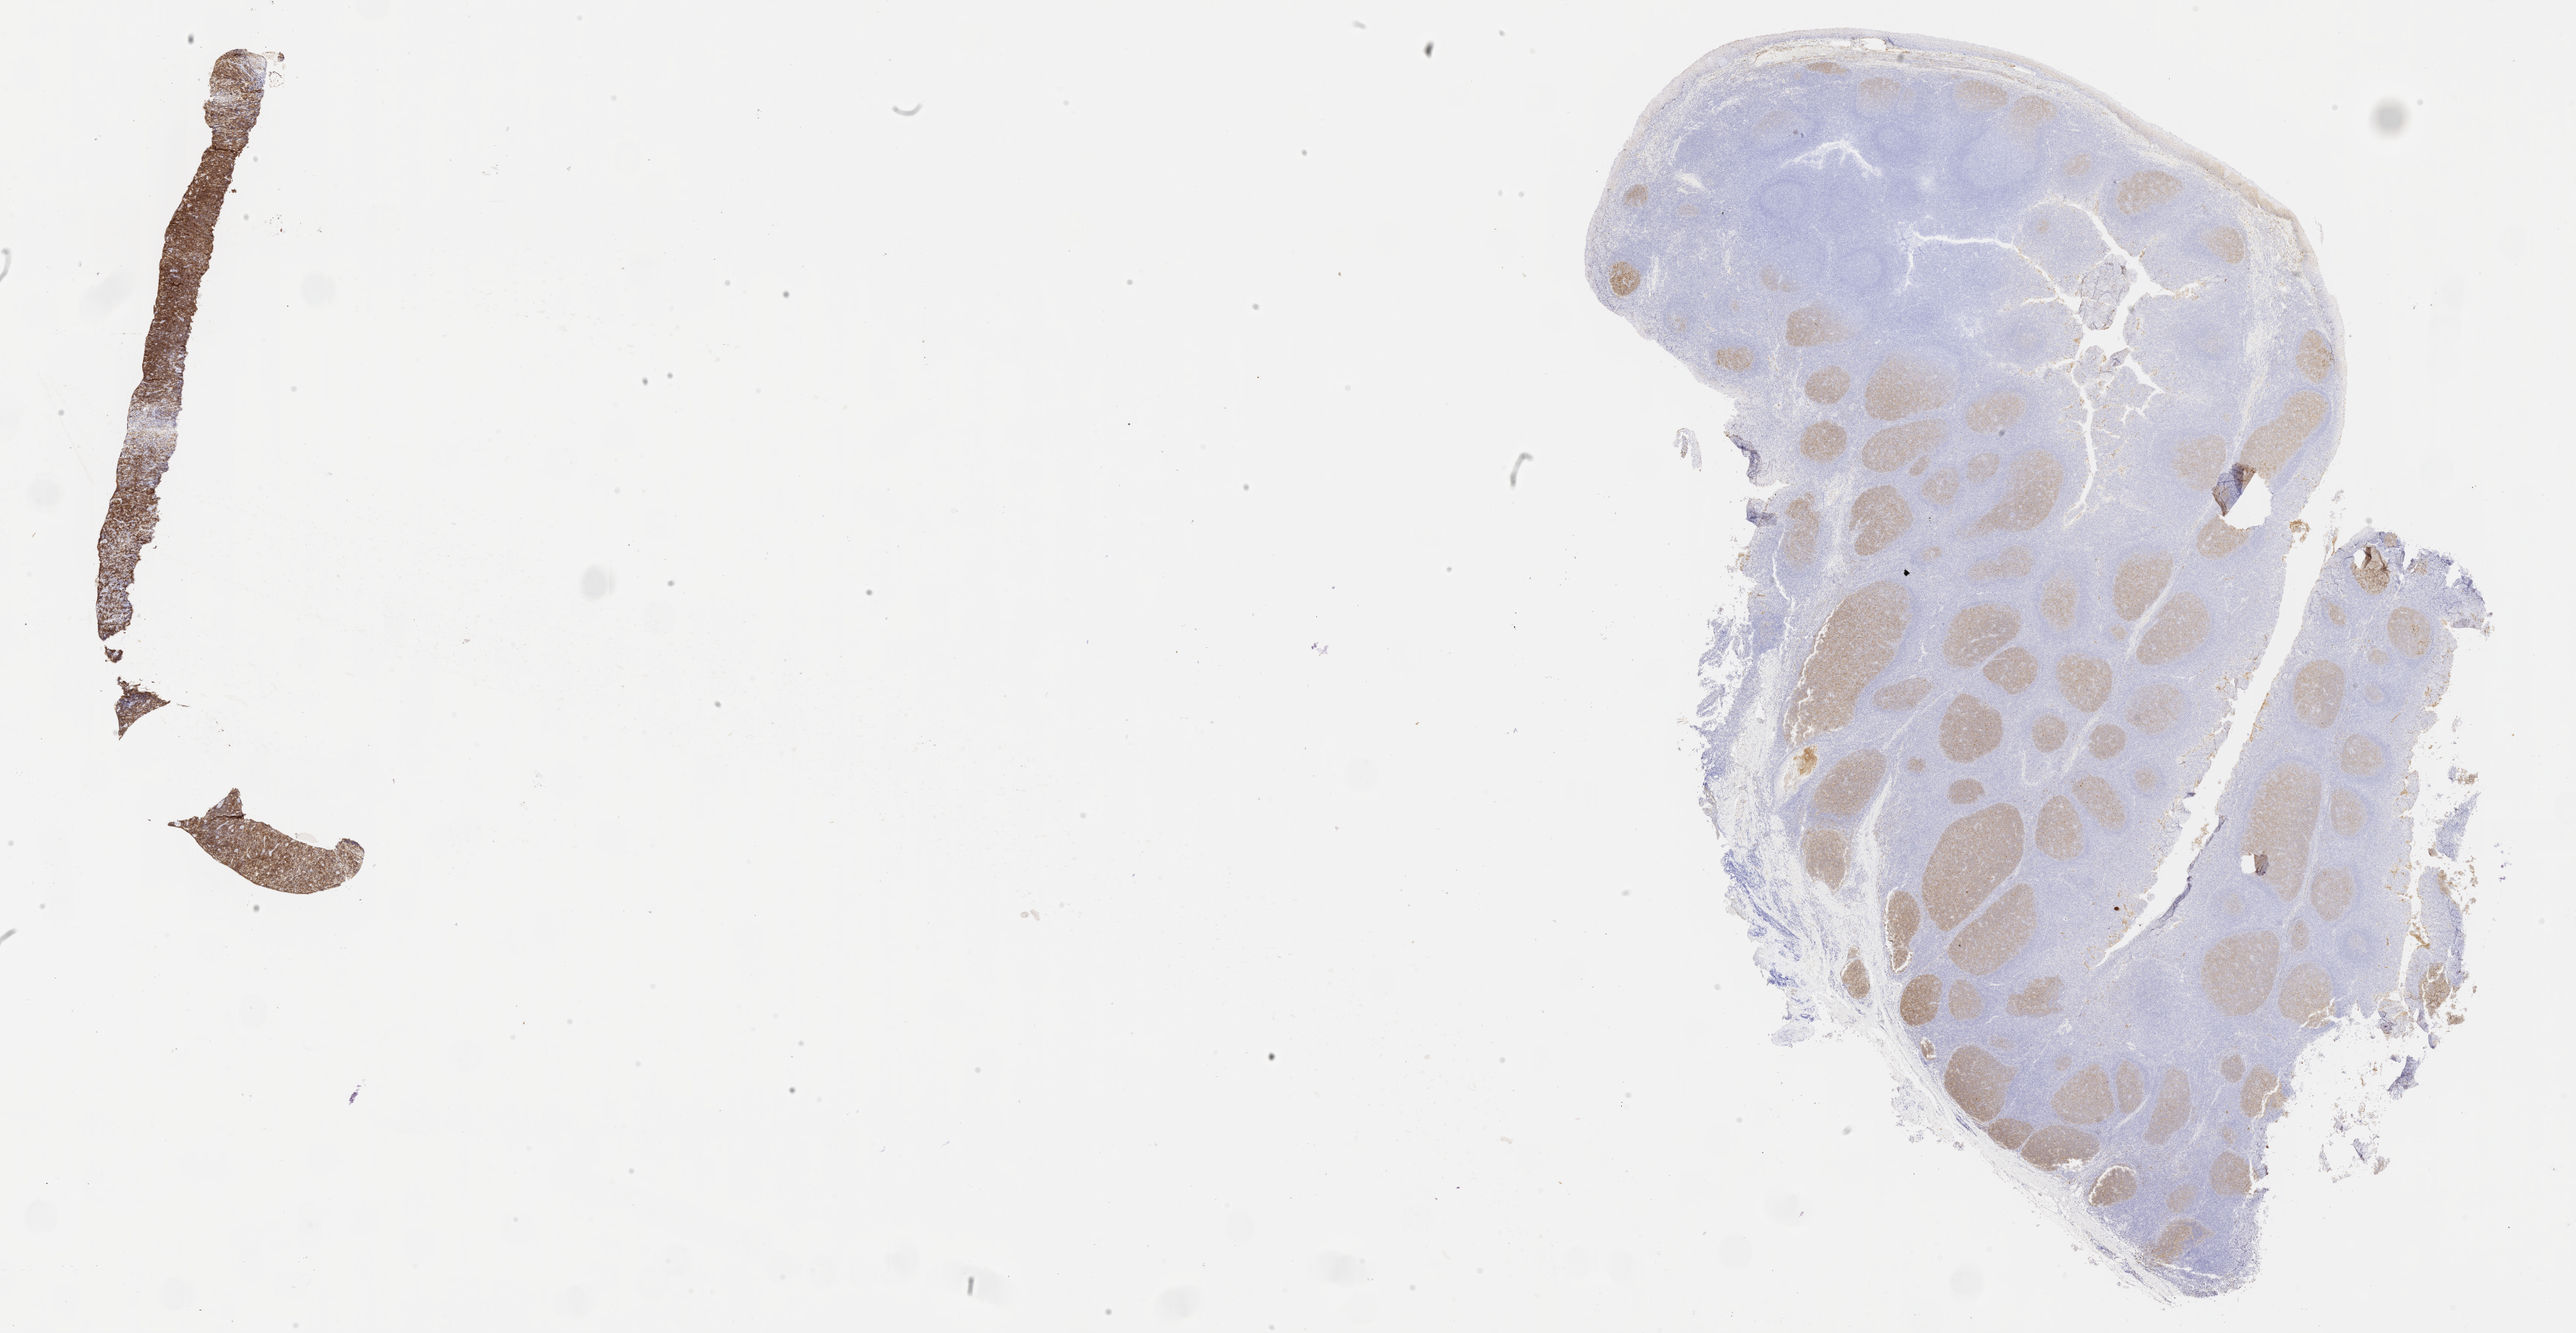
IHC for CD10, whole-slide image — whole scanned area (about 27.7 x 14.3 mm) shown as a low-resolution overview. Specimen: tumor tissue. Anatomic site: ovary. Patient: female, age at initial diagnosis 9 years.
Diagnosis: Burkitt lymphoma, NOS.